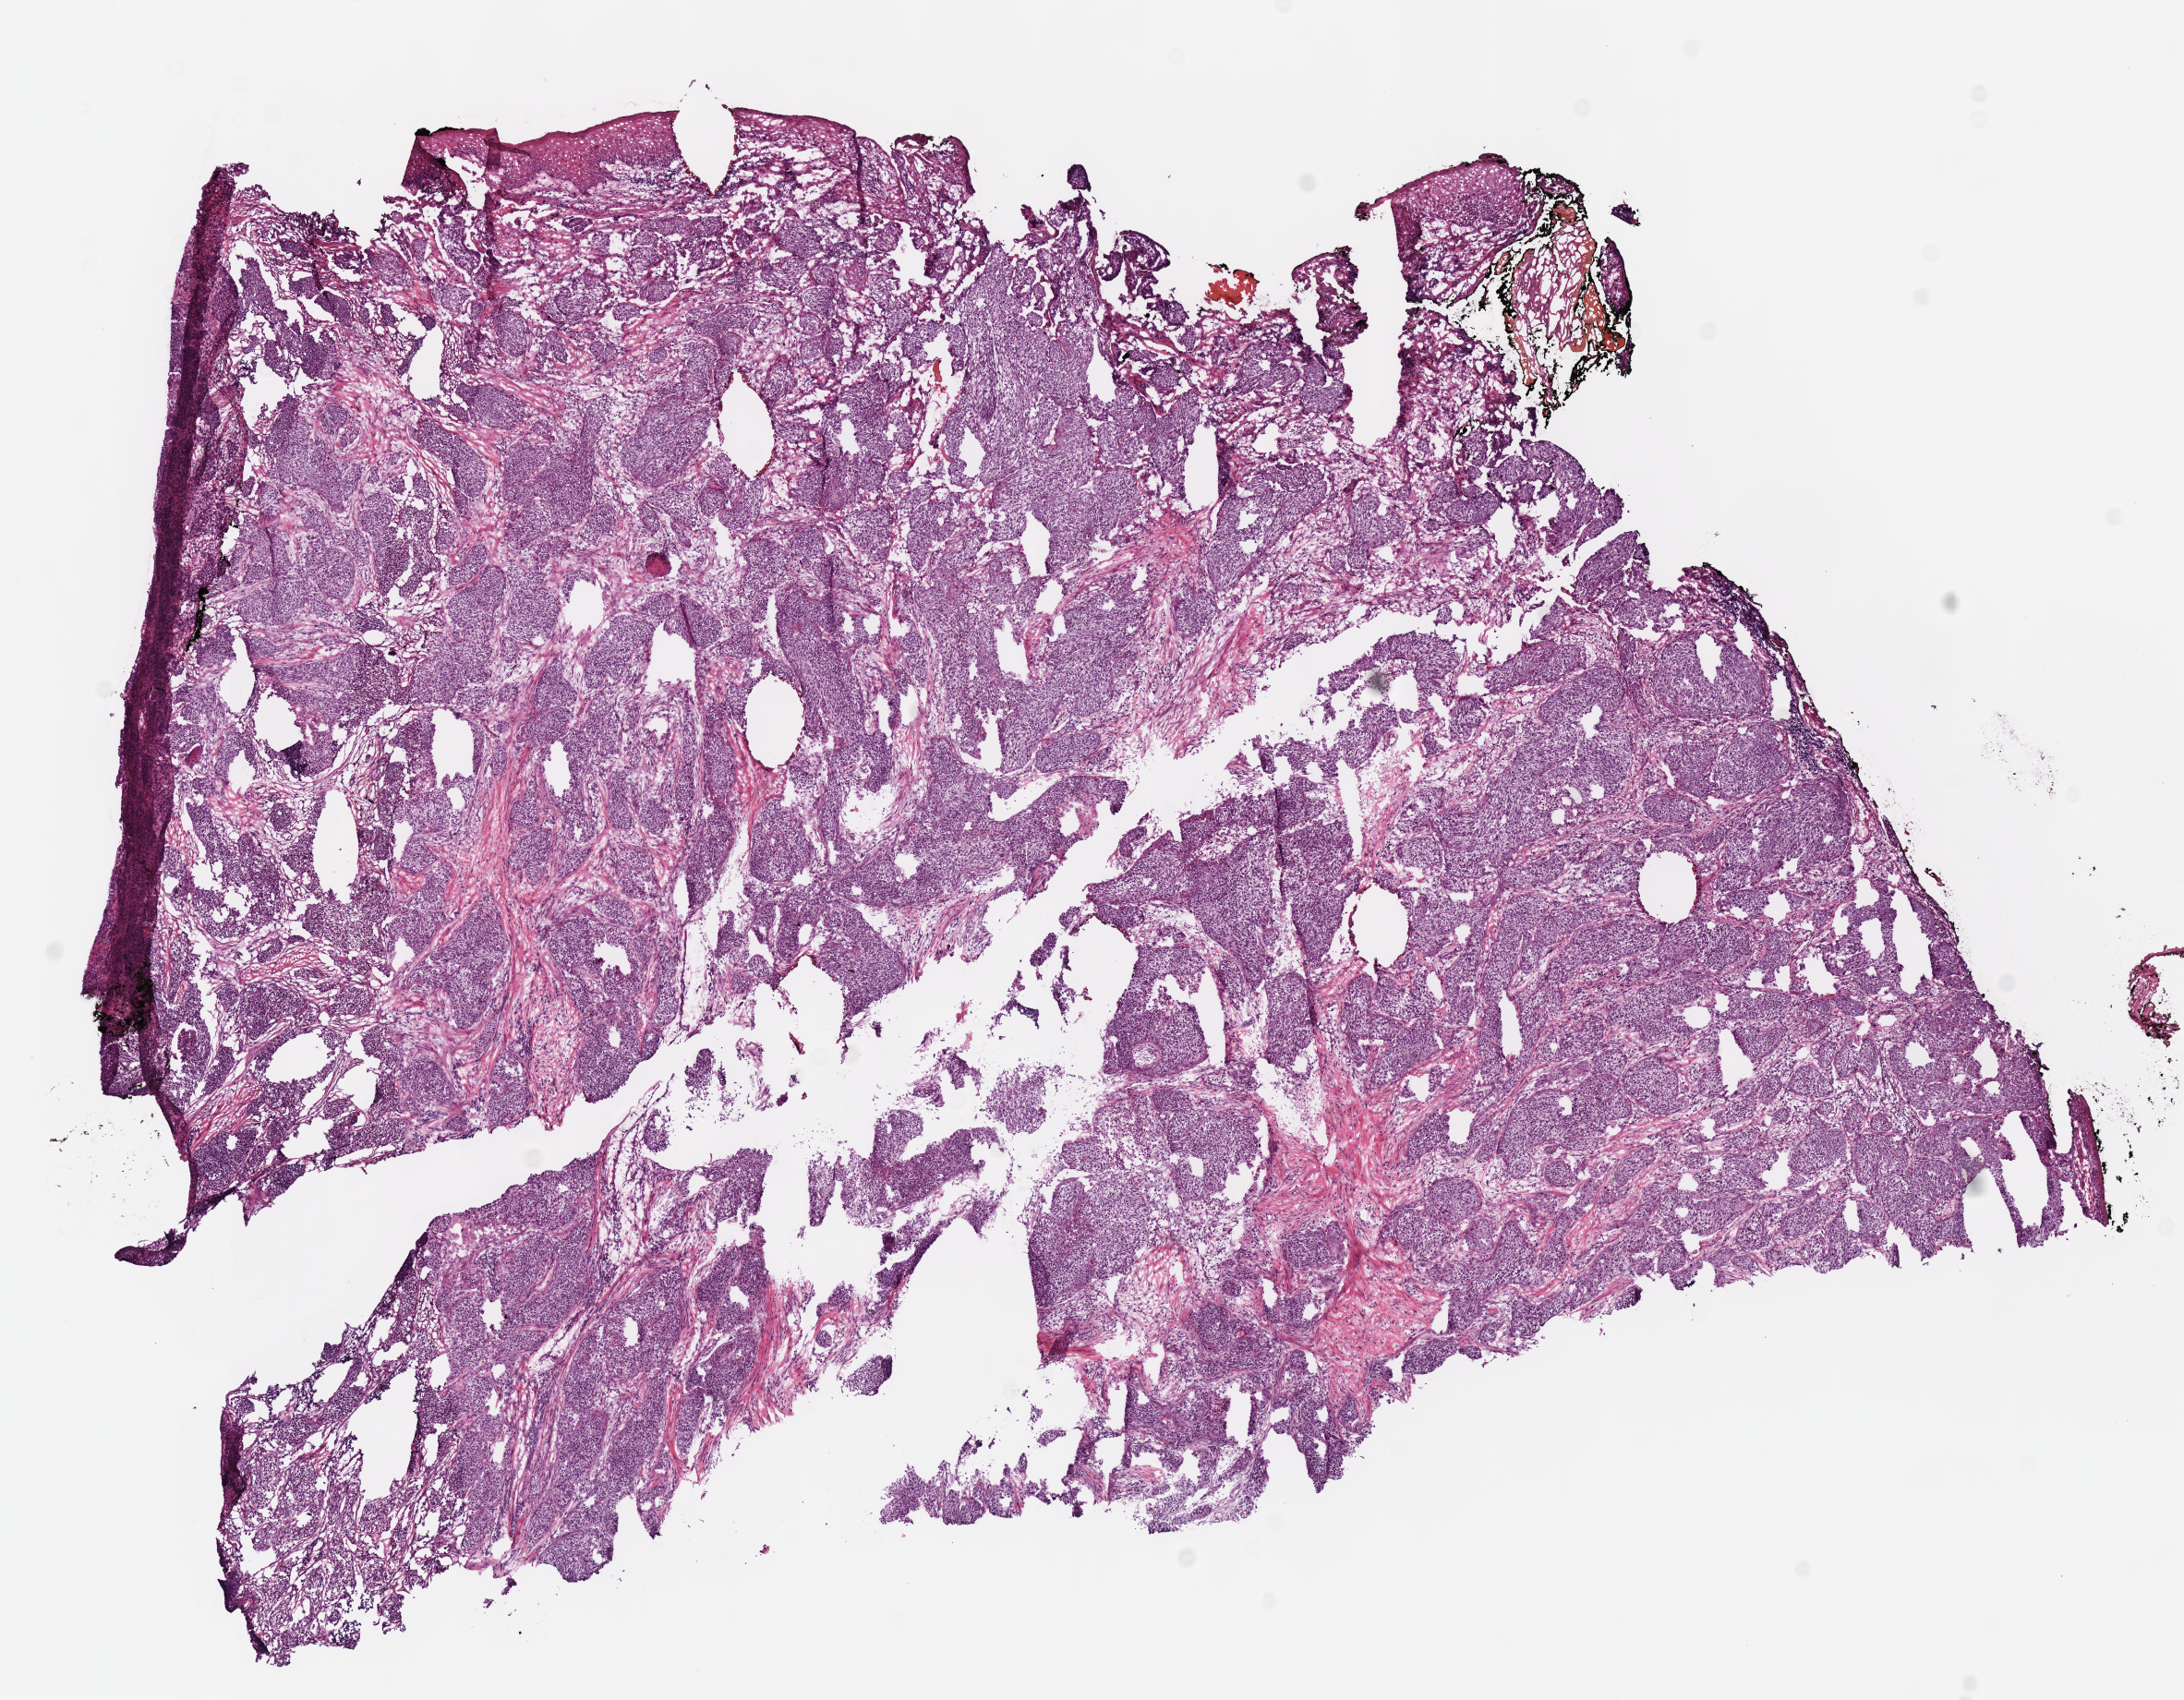
H&E-stained whole-slide image, shown as a low-resolution overview of the whole scanned area (about 9.3 x 7.2 mm, from a 40x scan). Frozen section from the top of the tissue portion. Primary tumour sample from the head and neck. Male, age 69 years at initial diagnosis. Pathologist review of this section (percent, as recorded): tumour nuclei 80%, necrosis 0%.
Histologic diagnosis: Squamous cell carcinoma, NOS (oropharynx, NOS).